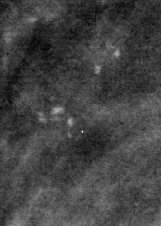
Cropped region of a digitized screen-film mammogram centred on a radiologist-marked abnormality, right breast, MLO view.
Marked abnormality: calcifications, morphology pleomorphic, distribution clustered; BI-RADS assessment category 4; subtlety rating 3 on a 1 (subtle) to 5 (obvious) scale; pathology (as recorded): malignant.